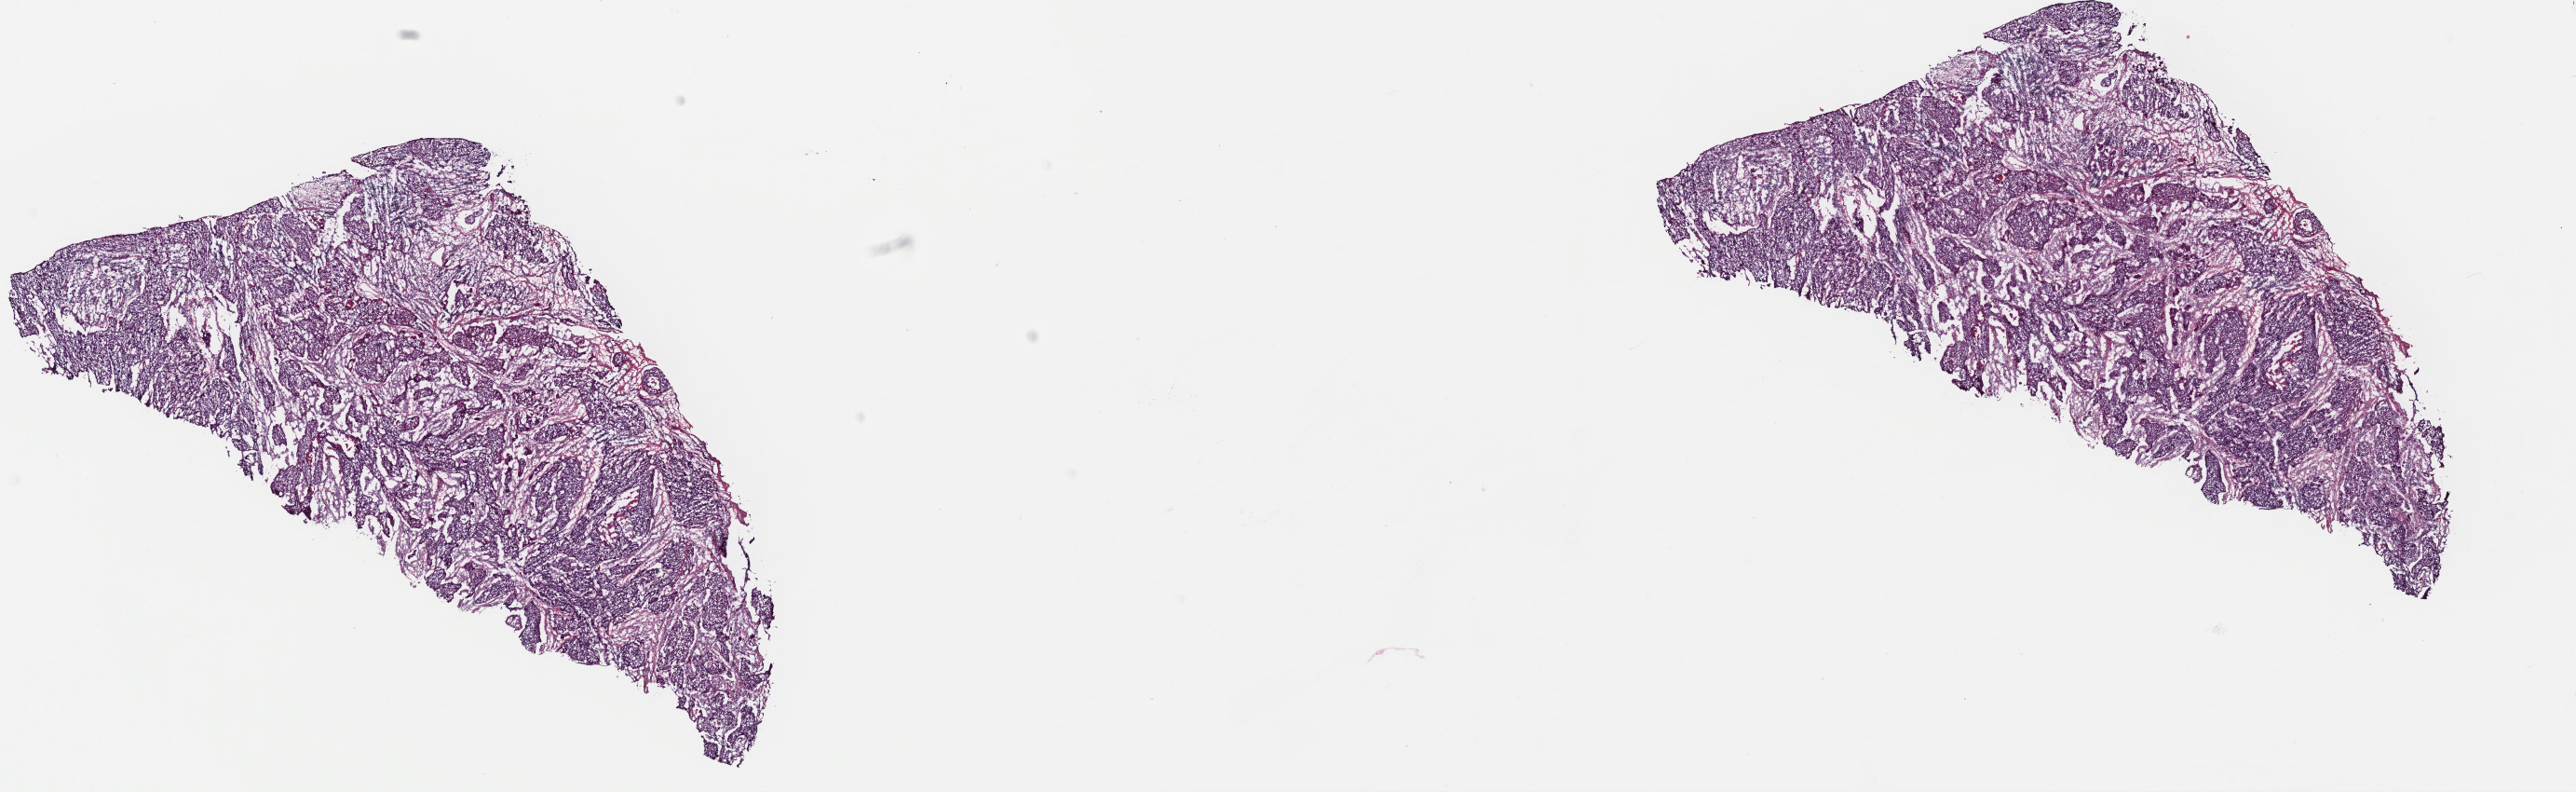
Whole-slide histology image, H&E — shown as a low-resolution overview of the whole scanned area (about 21.9 x 6.7 mm, slide scanned at 40x). Frozen section. Primary tumour sample from the cervix. Female patient; age at initial diagnosis 31 years. Histologic grade: G2 (moderately differentiated). Slide review estimates, as recorded: tumour cells 90%, tumour nuclei 70%, normal cells 10%, stromal cells 0%, necrosis 0%. Infiltration values recorded for this section: lymphocyte infiltration 5%, monocyte infiltration 5%, neutrophil infiltration 1%.
FIGO stage: IIIB. Histologic diagnosis: Squamous cell carcinoma, NOS.